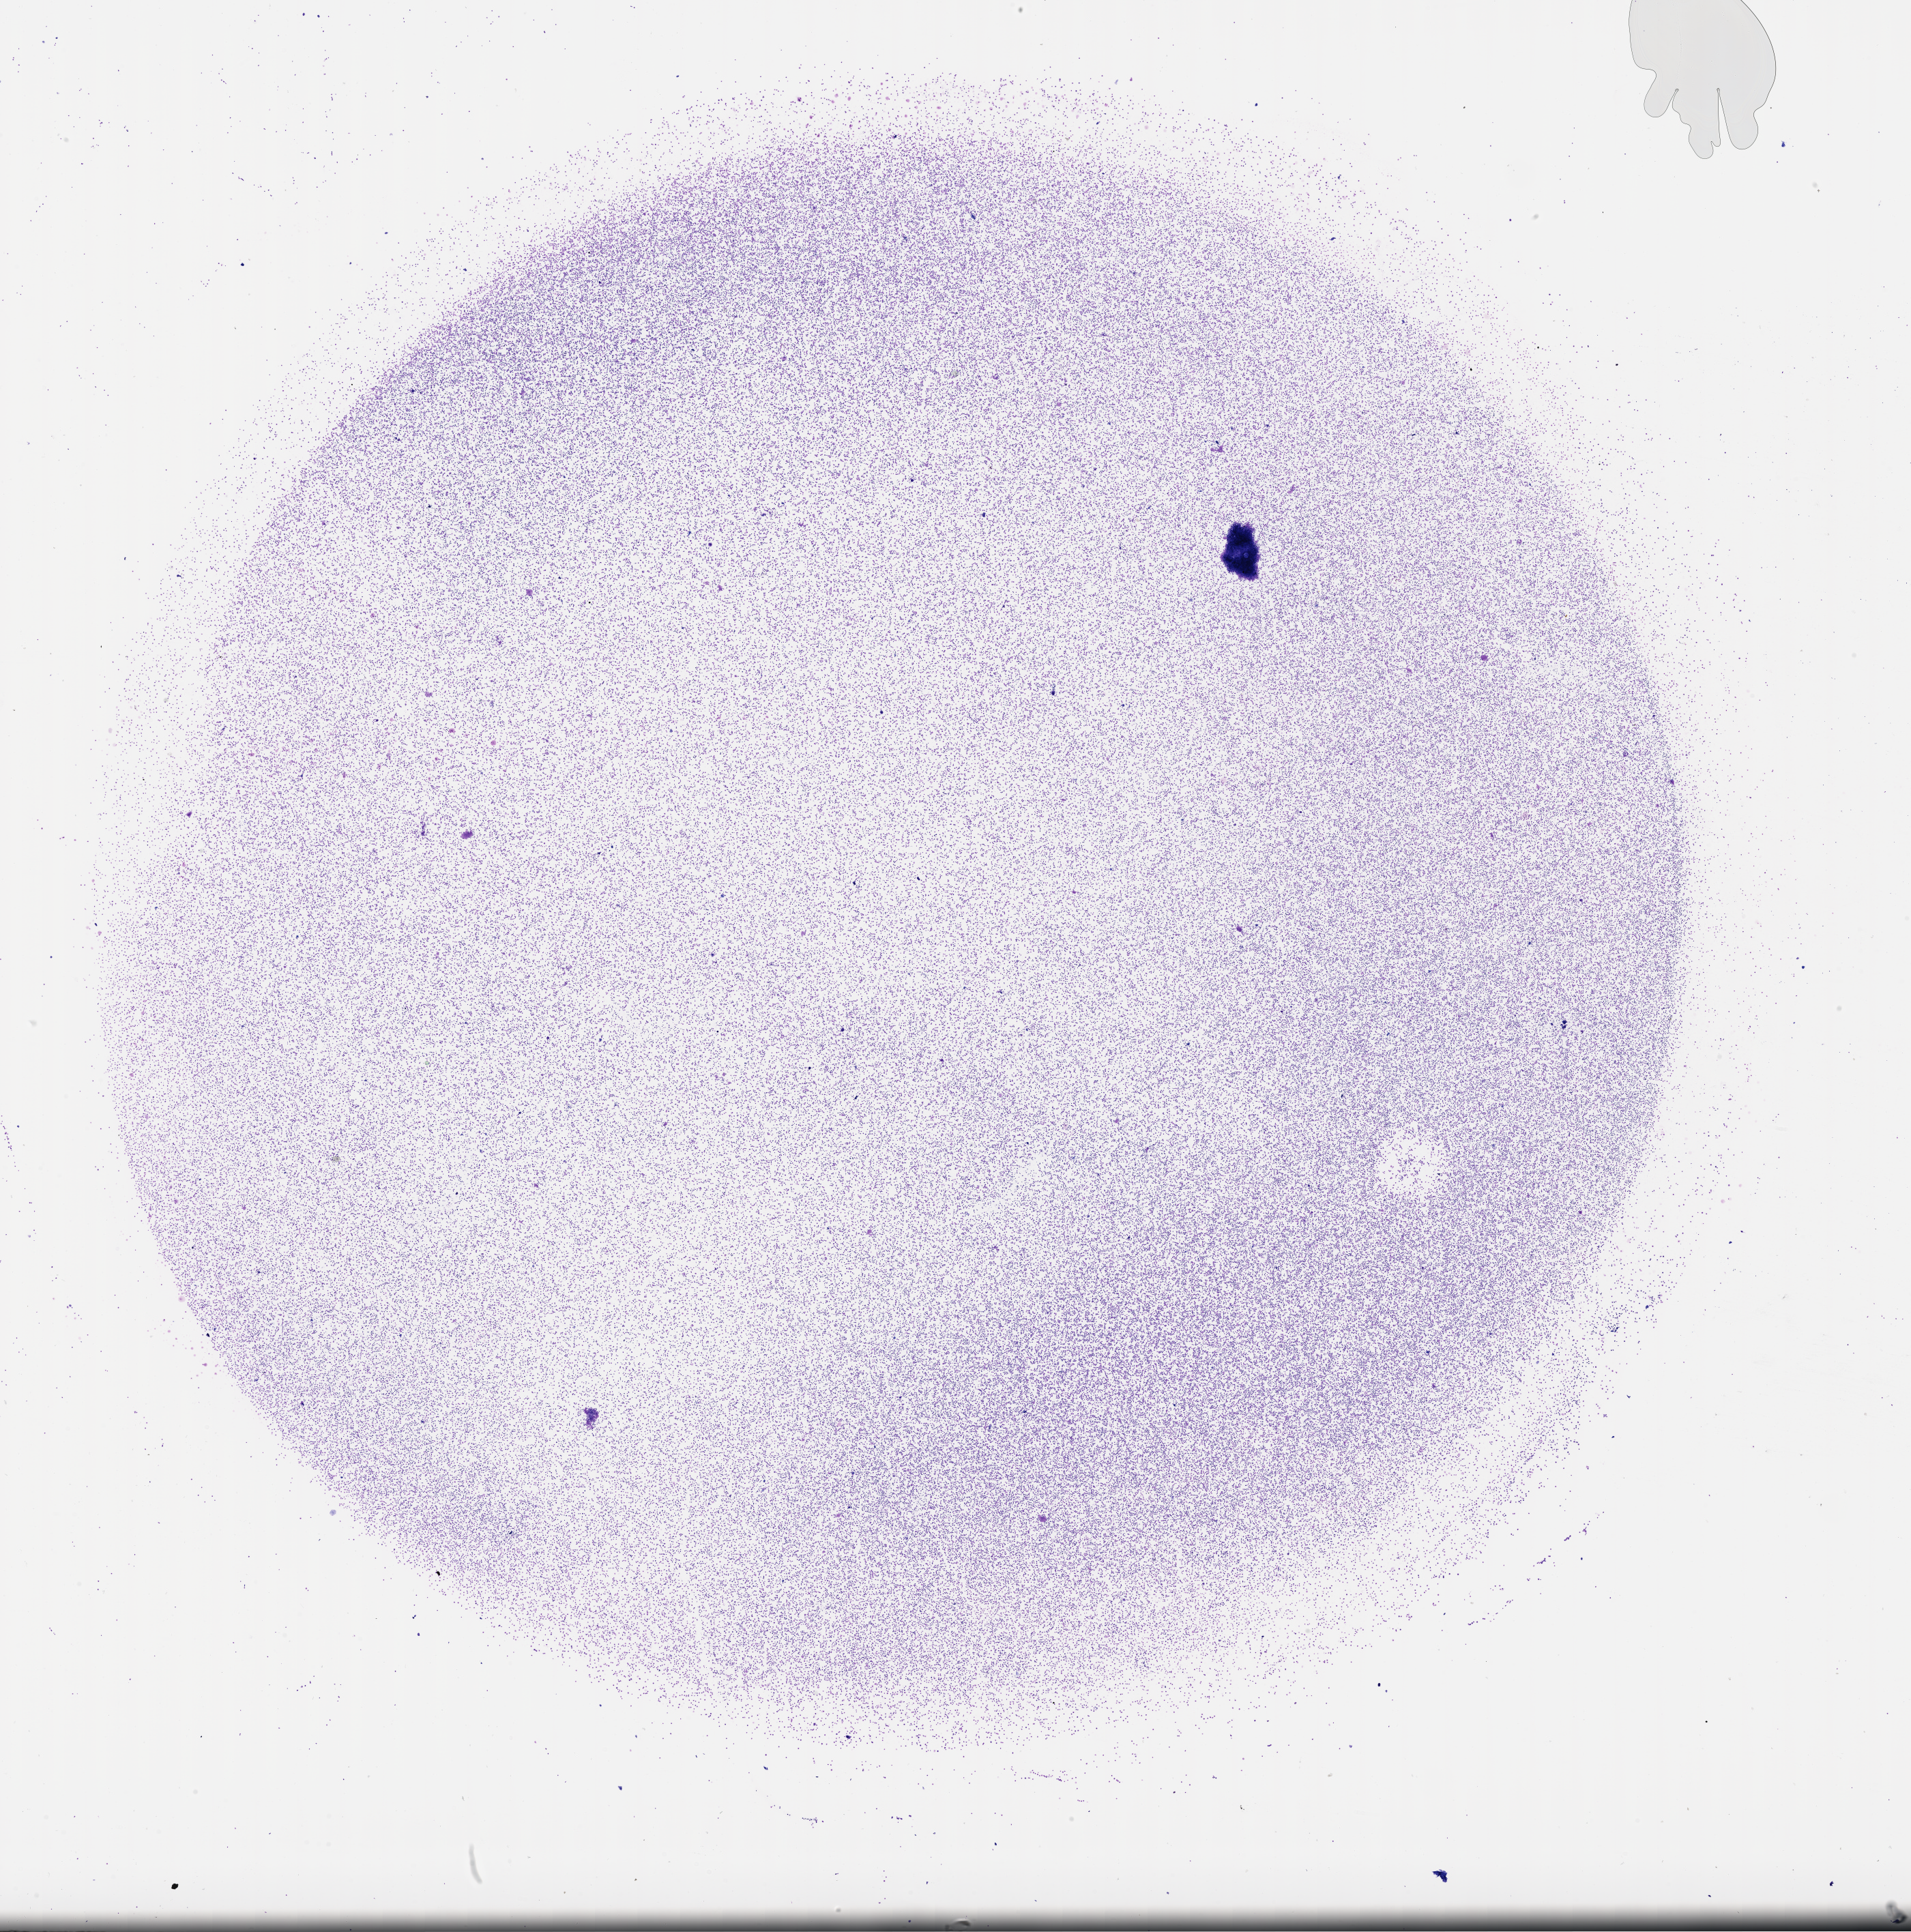
H&E whole-slide image, shown as a low-resolution overview of the whole scanned area (about 22.6 x 22.9 mm), bone marrow (leukaemic) sample. 50-year-old female patient.
Diagnosis: Acute Myeloid Leukemia.